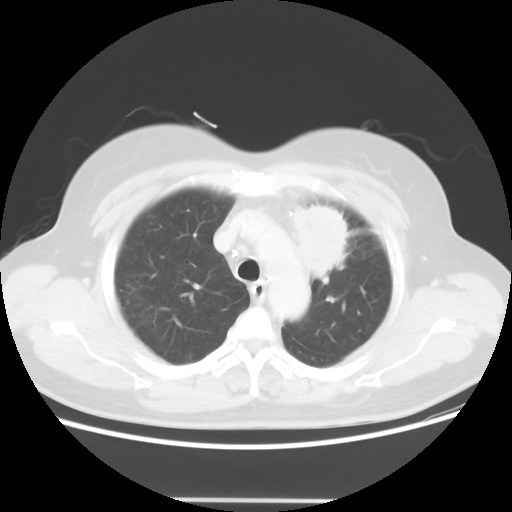
Chest CT, one axial slice. Slice 42 of 52 in the series (ordered by position). Reconstruction kernel STANDARD. Lung window (W 1500 / L -600 HU). 512 × 512 image matrix, field of view 382 × 382 mm. Female patient, age 52 years. Case-level facts recorded for this patient, not image findings: clinical TNM (as recorded): T2 N3 M0.
Outlined on this slice (bounding box drawn by a radiologist):
- lung tumour (recorded histology: adenocarcinoma): bounding box <285,203,355,278> (left, top, right, bottom; pixels)